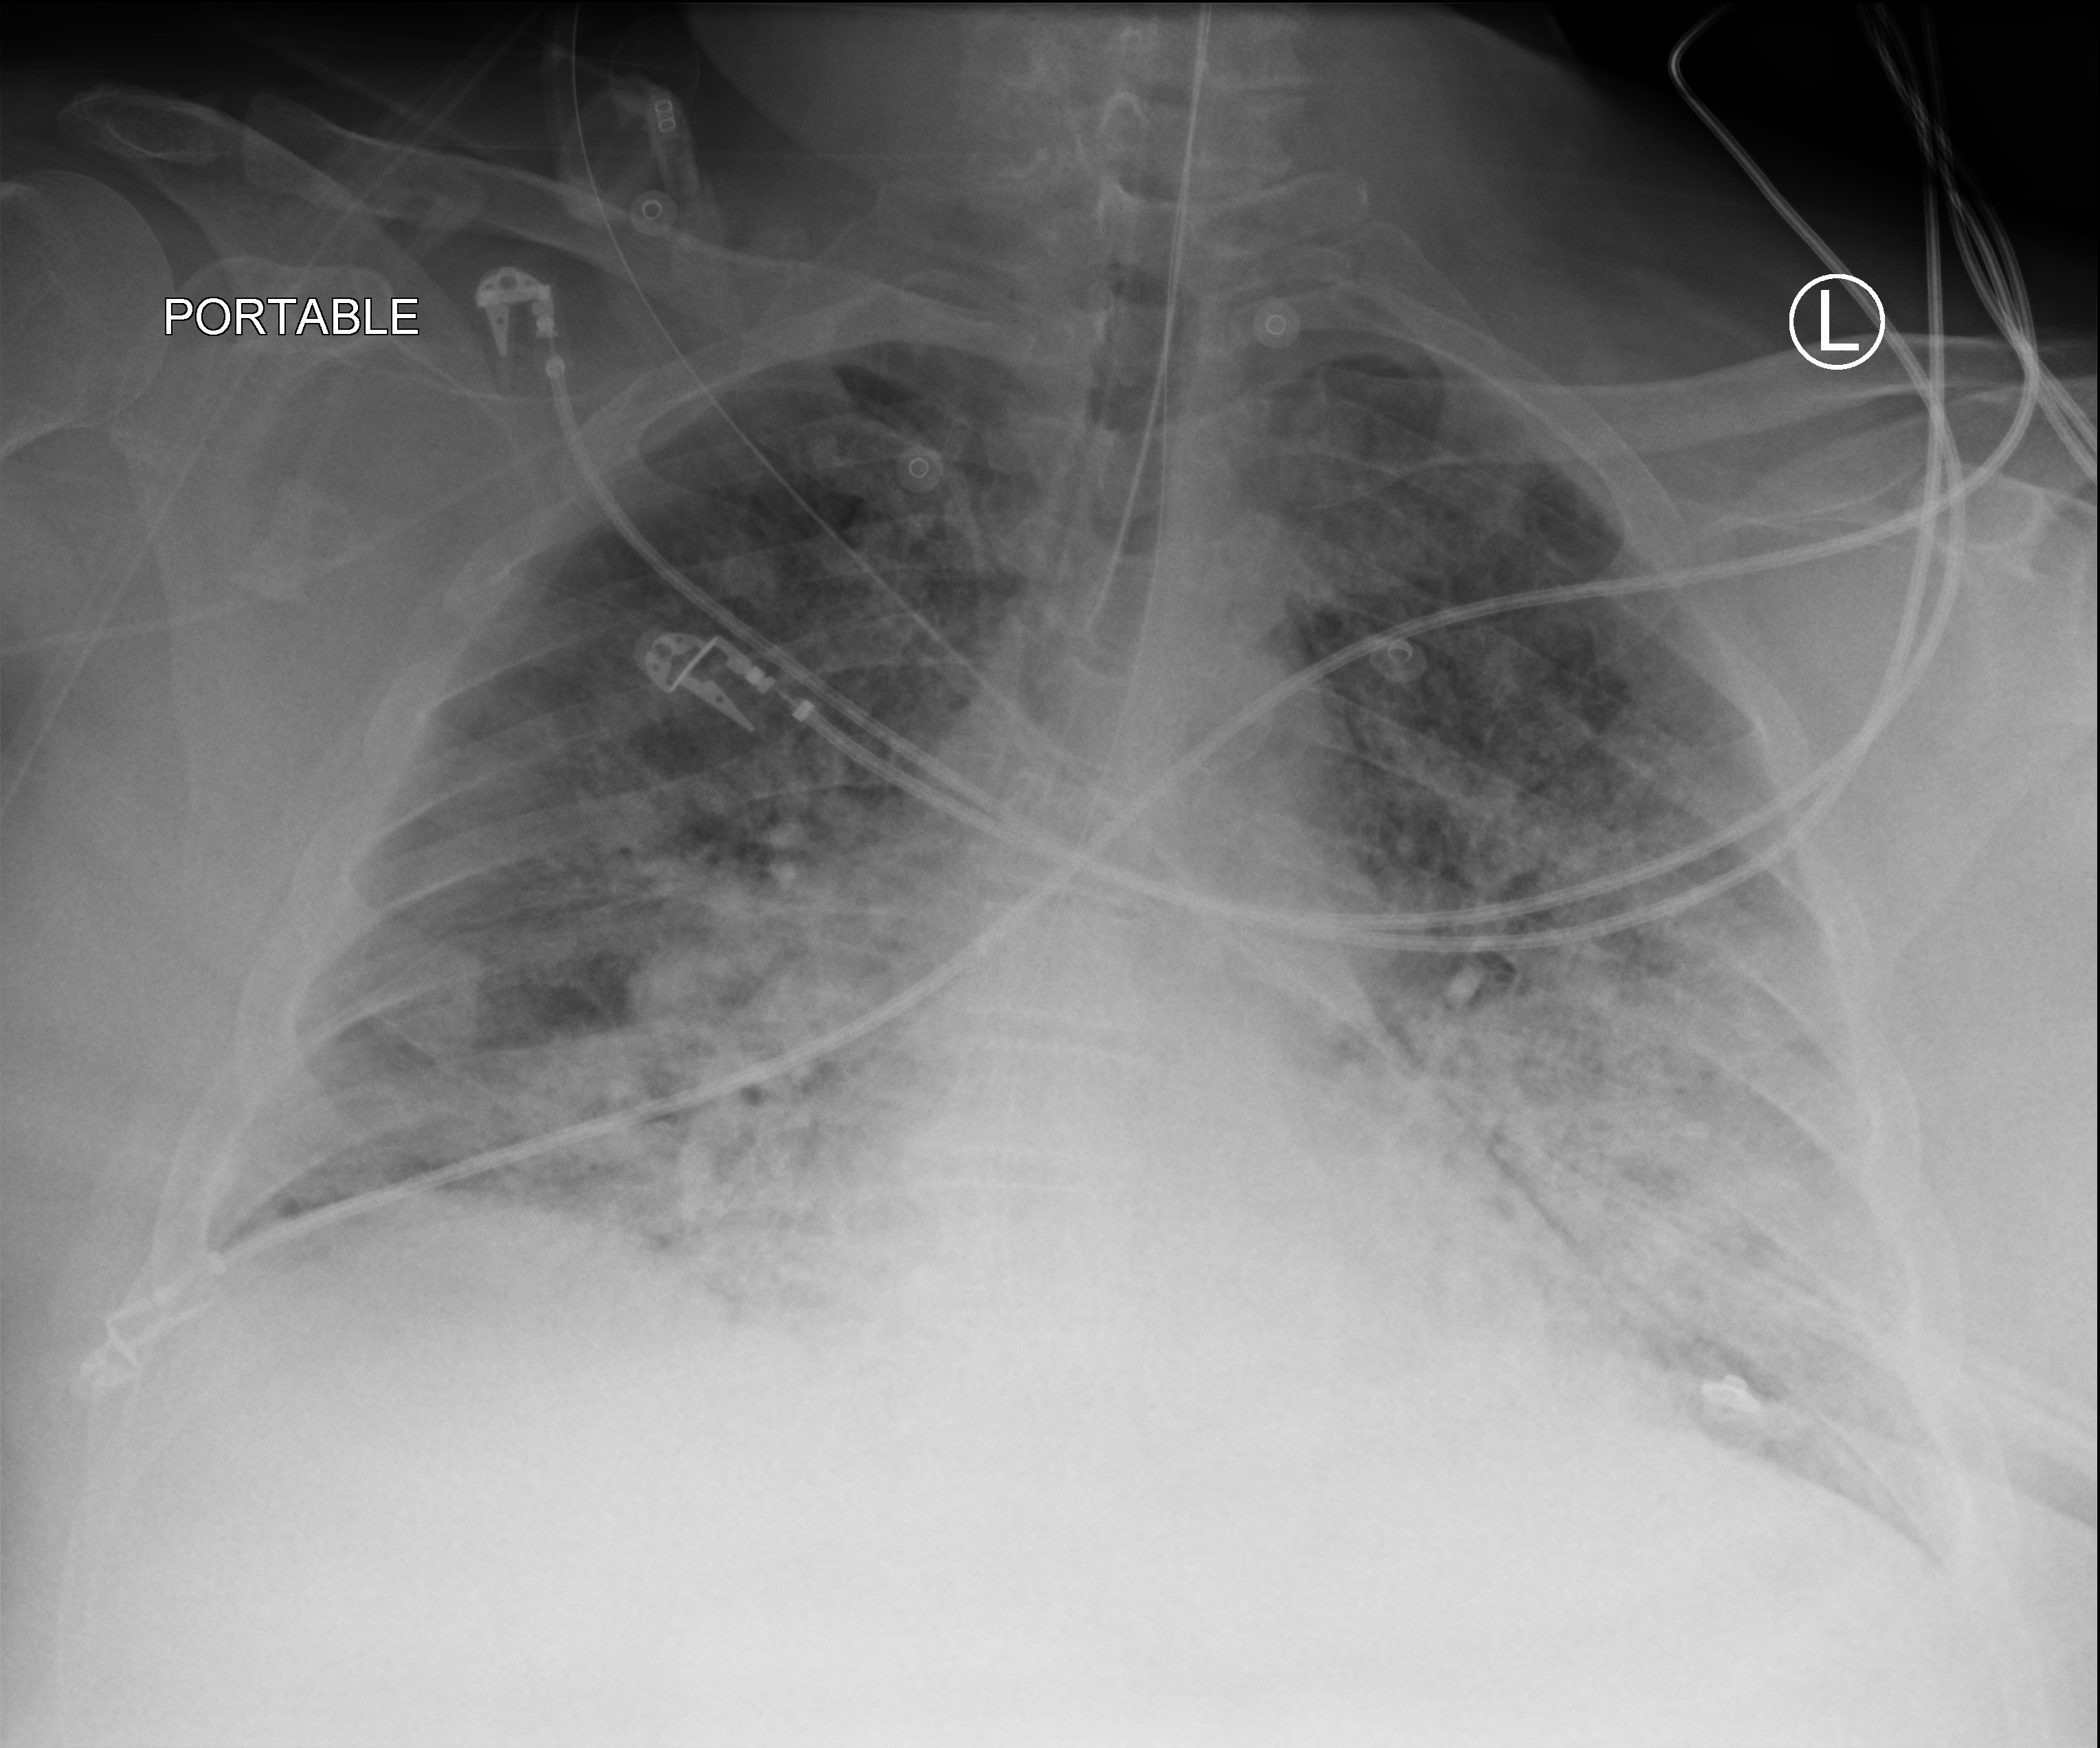
Portable chest radiograph, anteroposterior (AP) projection. Male patient hospitalised with COVID-19, age 60–74 years.
From the hospital-stay record, not from the radiograph (when in the stay this image was taken is not recorded): admitted to intensive care during this hospital stay: yes; hypertension (admission record): yes; mechanically ventilated during this hospital stay: yes.